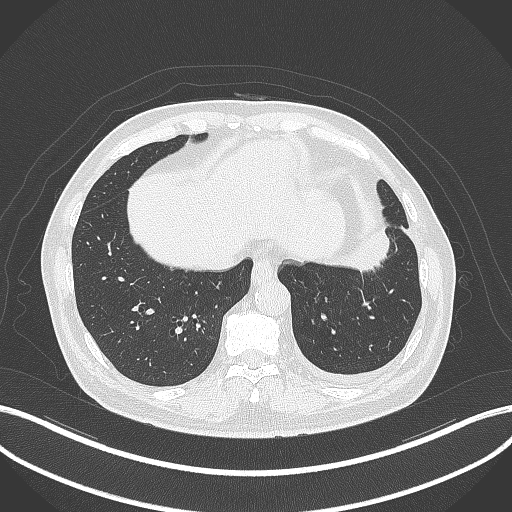
Chest CT, one axial slice; position 87 of 230 along the scan axis; reconstruction kernel B70f; 120 kVp; lung window (W 1500 / L -600 HU); 1 mm slice thickness; 512 × 512 image matrix. Patient: male, 68 years. Case-level facts recorded for this patient, not image findings: clinical TNM (as recorded): T2b N0 M0.
Annotated regions visible in this slice (bounding box drawn by a radiologist):
- lung tumour (recorded histology: squamous cell carcinoma): bounding box (x1, y1, x2, y2) in pixels: (337, 220, 398, 282)